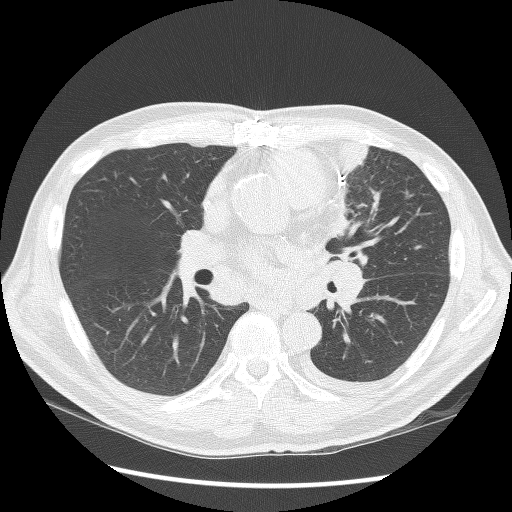
Low-dose screening chest CT, axial slice, second annual screen, lung window (W 1500 / L -600 HU), lung (sharp) reconstruction kernel (BONE), 120 kVp, slice 61 of 136 in the series. Male participant, aged 64 years at enrolment. Former smoker at enrolment.
Expert-annotated lung lesion, bounding box <306,126,396,277> (left, top, right, bottom; pixels). Screening reader's record for this exam: no non-calcified nodule ≥4 mm recorded. Official screen result: positive, other. Participant outcome: lung cancer diagnosed 24 days after this screen — small cell carcinoma, NOS, left upper lobe, stage IV (AJCC 6th edition), 100 mm at pathology.